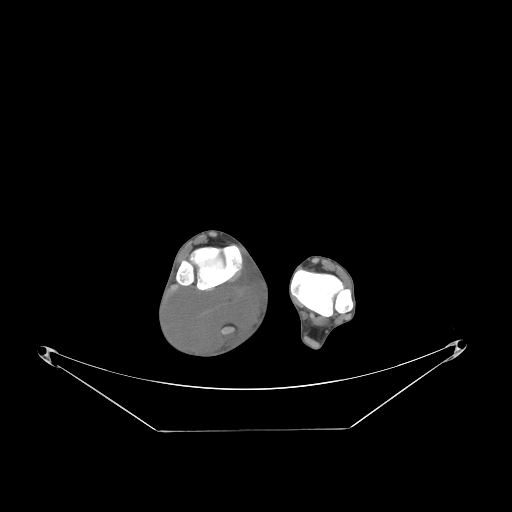
CT of an extremity soft-tissue mass (from a PET/CT study), one axial slice. Slice 48 of 267 in the series (ordered by position). 140 kVp. Soft-tissue window (W 400 / L 40 HU). 3.75 mm slice thickness. 512 × 512 image matrix. Male patient. From the clinical record (not read from this slice): histological type: liposarcoma - round cell; grade: high; site of the primary tumour: right calf.
Outlined on this slice (expert contour drawn on MRI and transferred to this co-registered scan by the dataset authors):
- gross tumour volume (mass): bounding box [x1, y1, x2, y2] px = [167, 276, 261, 355]